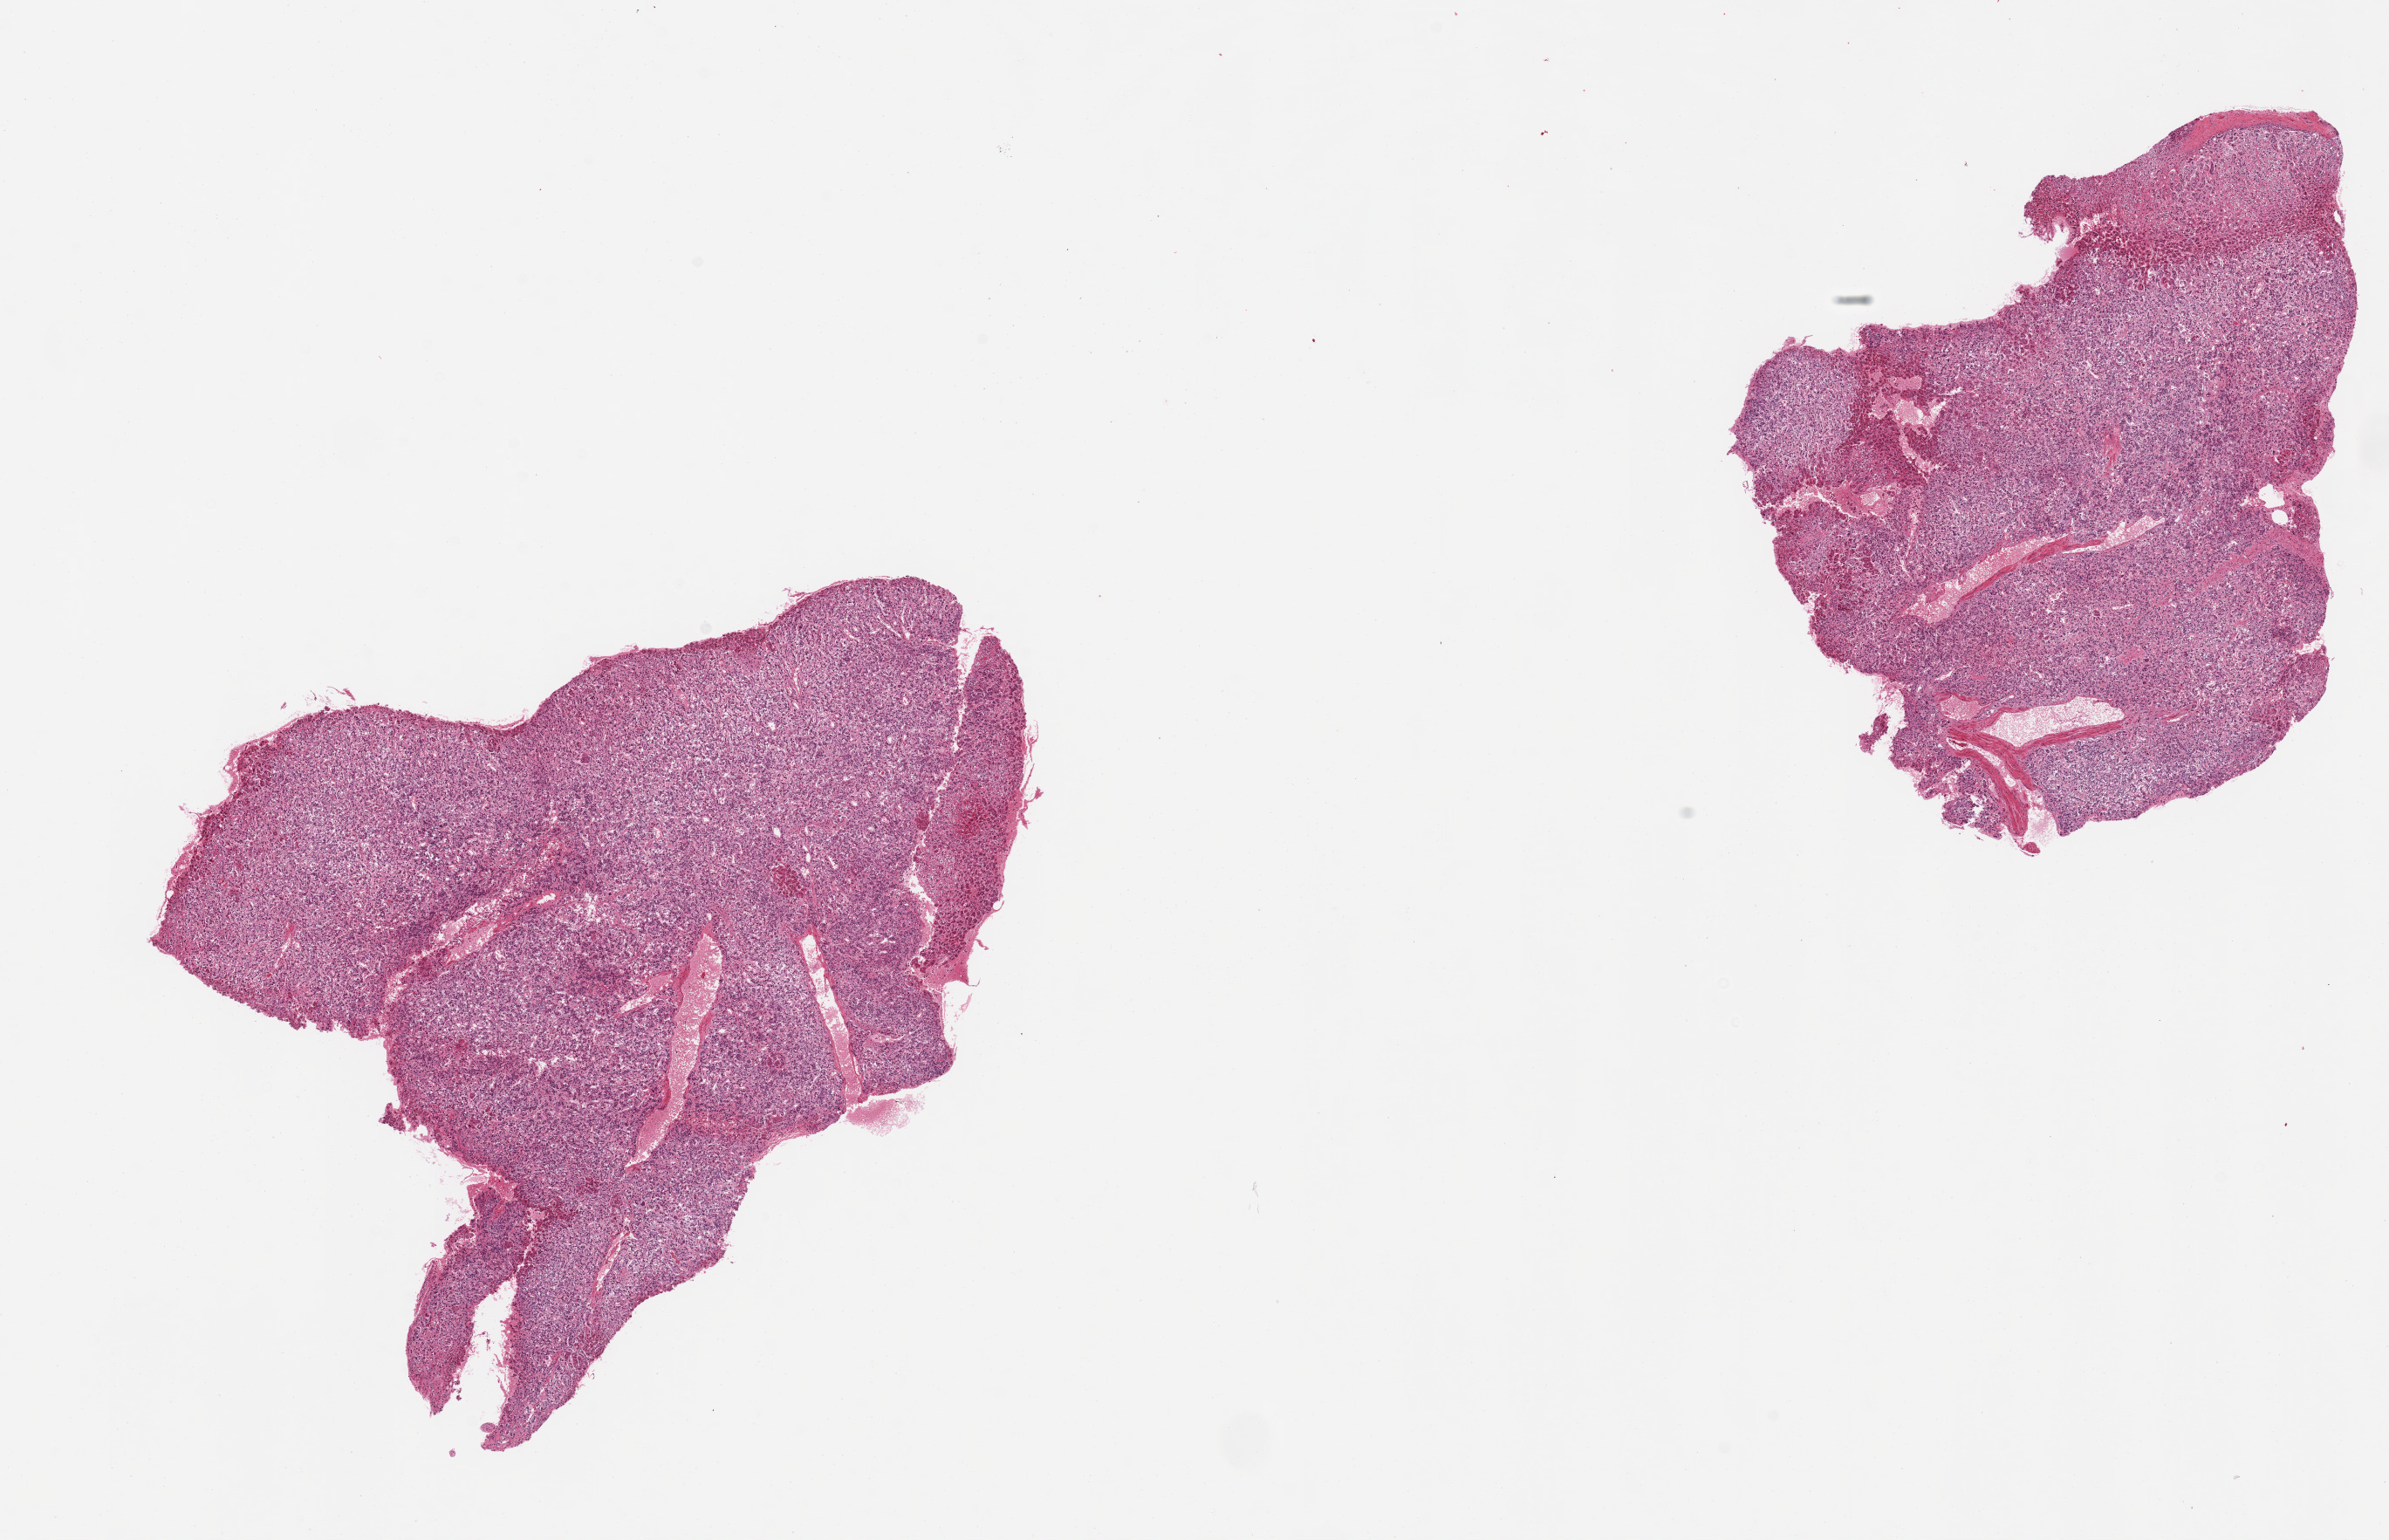
Whole-slide image, haematoxylin and eosin stain, shown as a low-resolution overview of the whole scanned area (about 21.7 x 14.0 mm, slide scanned at 20x), PAXgene-fixed paraffin-embedded (PFPE) section, target tissue: adrenal gland, donor tissue sample.
Pathologist's review note for this sample: 2 pieces, all cortex, good specimens, minimal fat.